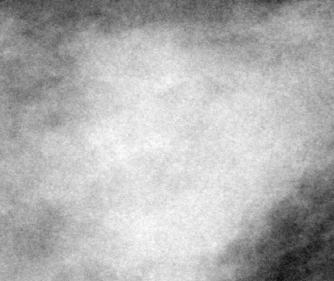
Crop from a digitized film mammogram around one marked abnormality, right breast, CC view, BI-RADS breast density category 4 (scale 1–4).
Marked abnormality: mass, shape irregular, margins obscured; BI-RADS assessment category 4; subtlety rating 3 on a 1 (subtle) to 5 (obvious) scale; pathology result (as recorded, not read from the image): malignant.